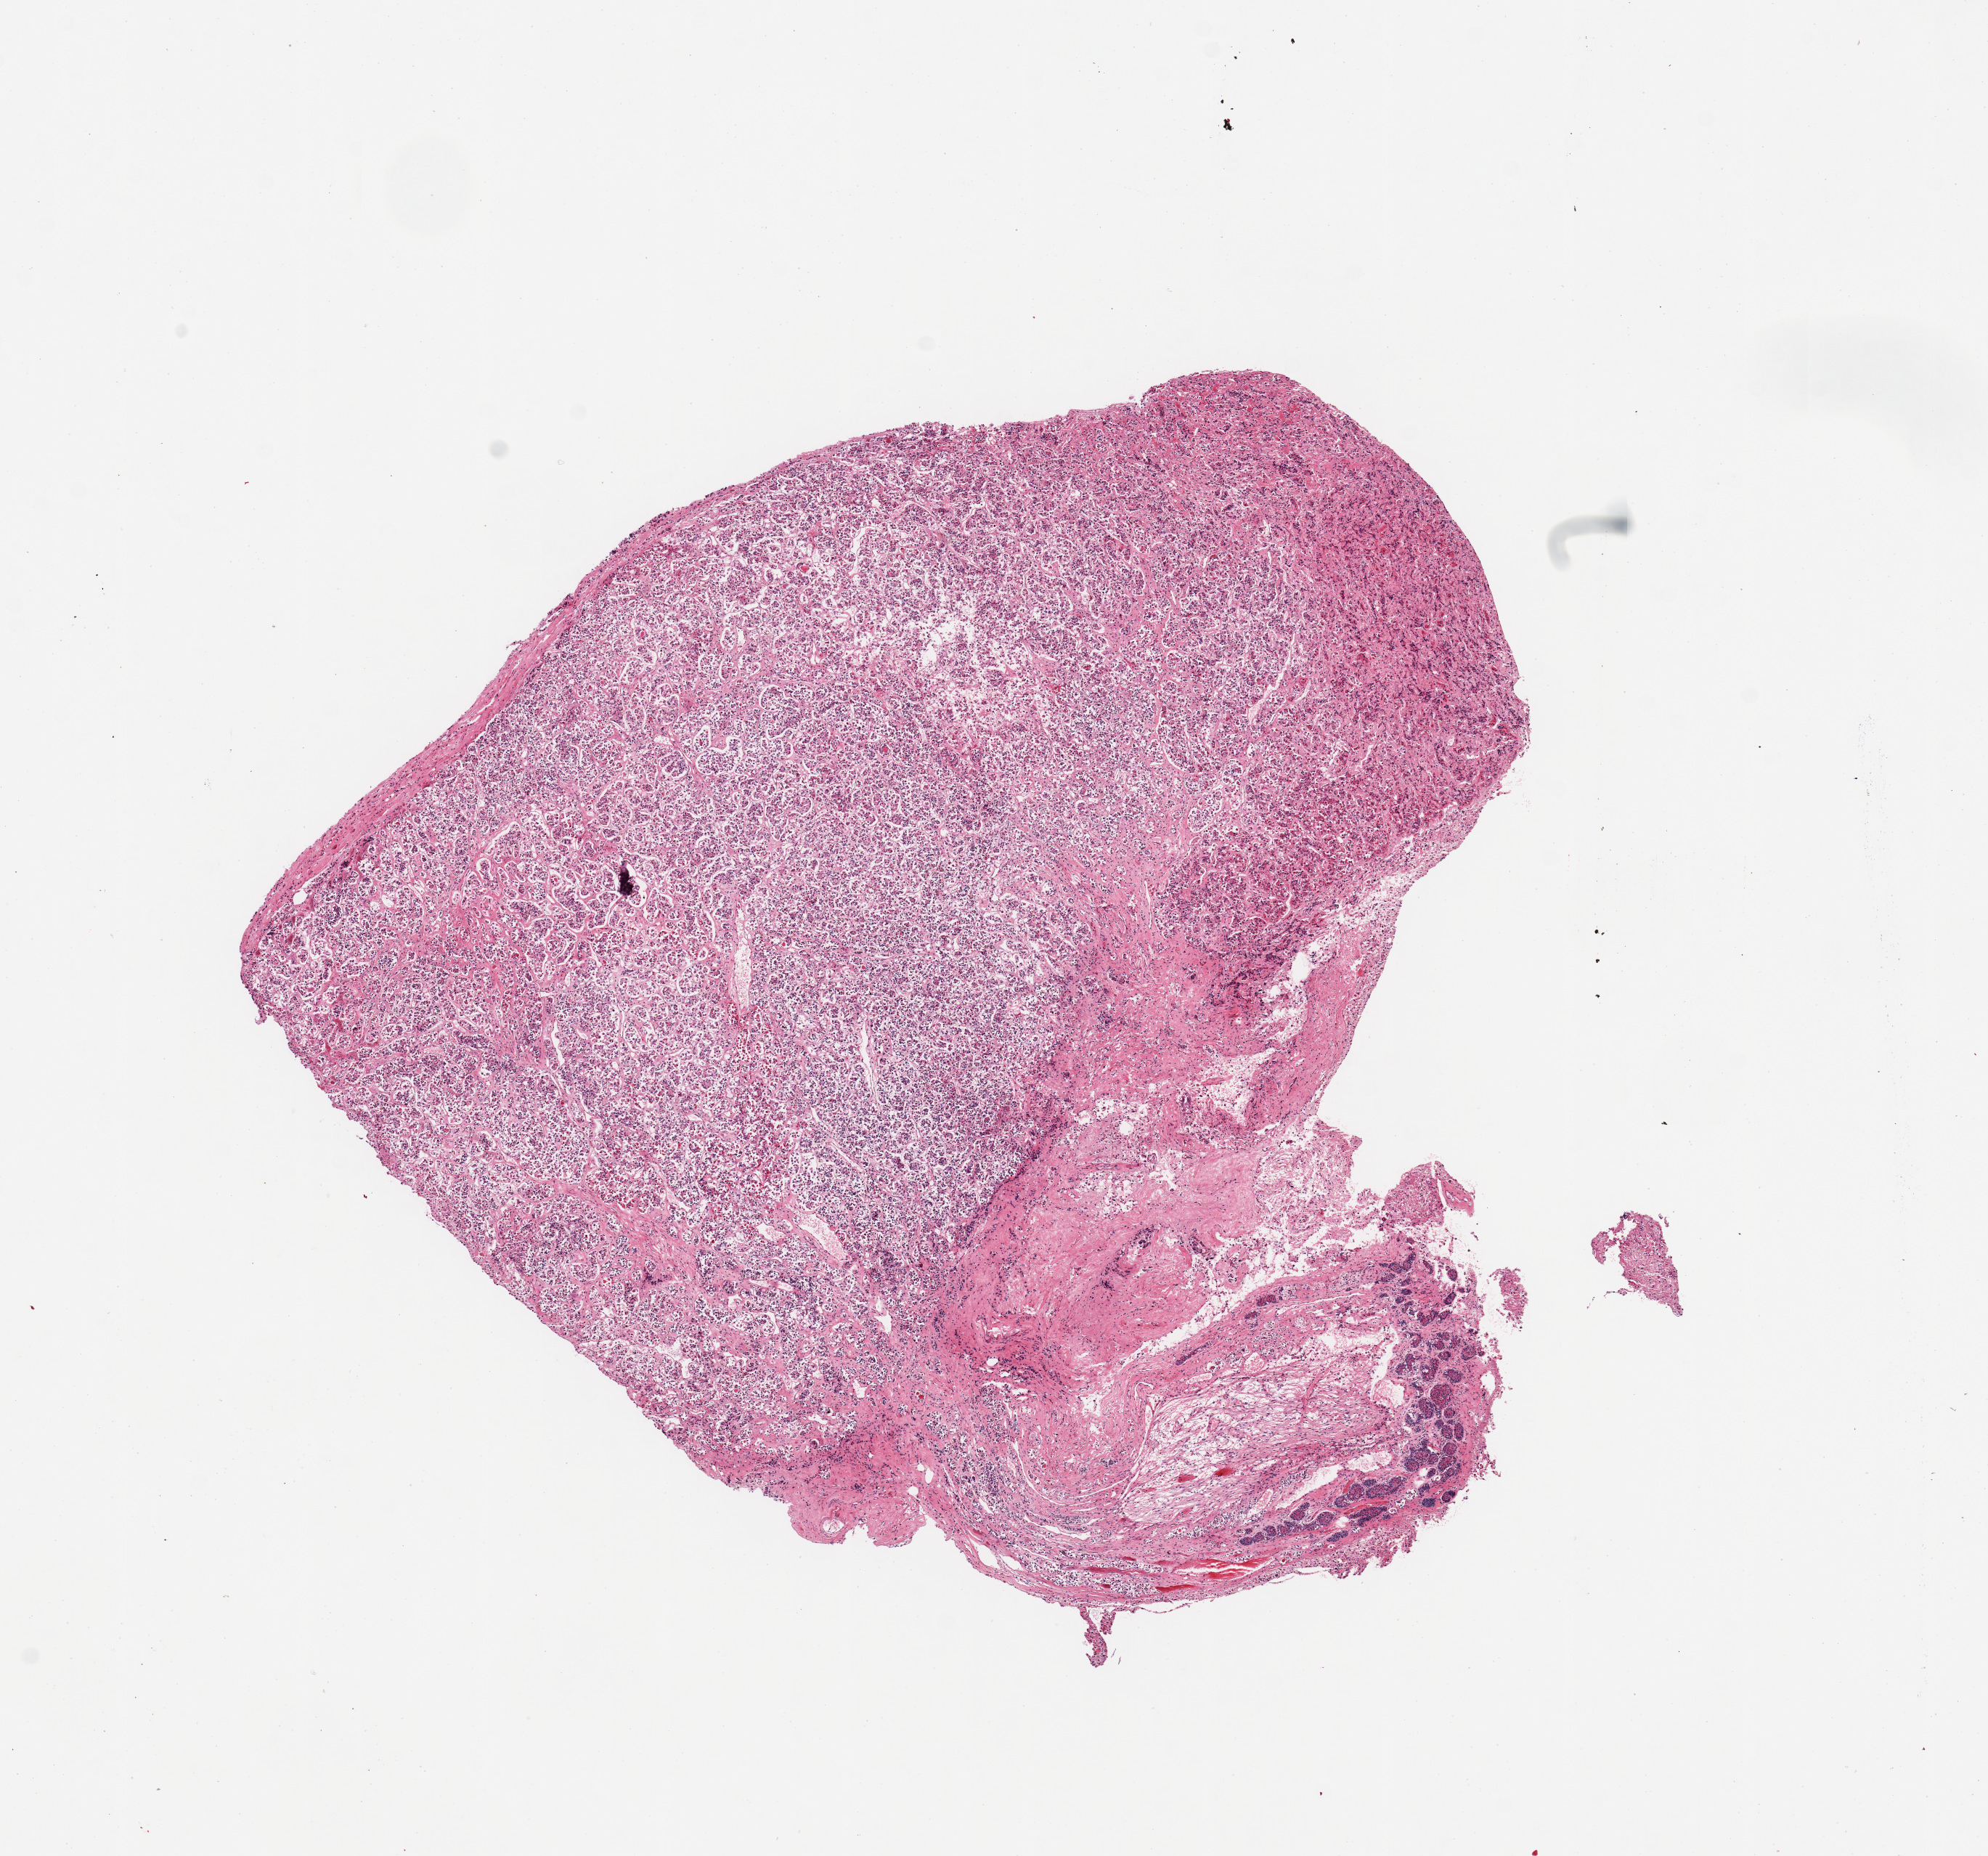
Whole-slide image, haematoxylin and eosin stain, a low-resolution overview of the entire scanned area, about 10.8 x 10.1 mm (slide scanned at 20x), PAXgene-fixed, paraffin-embedded tissue, target tissue: pituitary, tissue donor sample. Male donor.
Review note (as recorded): 1 piece; mostly adenohypophysis; 10% is neural.